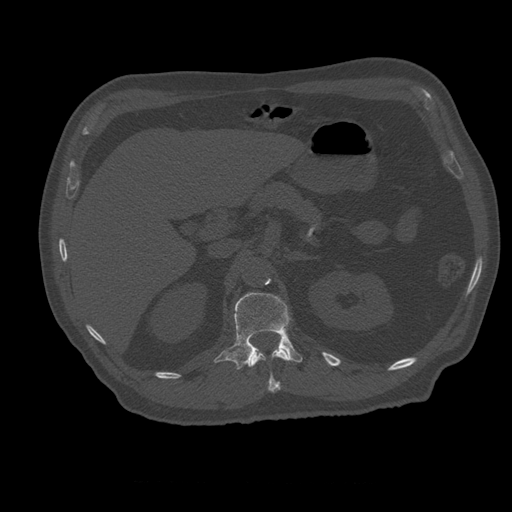
CT including the spine, one axial slice; position 245 of 399 along the scan axis; 120 kVp; bone window (W 1800 / L 400 HU); 1.25 mm slice thickness; 512 × 512 image matrix. Patient age 73 years. From the clinical record (not read from this slice): primary cancer: prostate.
Structures marked on this image (semi-automatically segmented with operator editing):
- L1 vertebra: bounding box (x1, y1, x2, y2) in pixels: (214, 293, 303, 370)
- T12 vertebra: (249, 347, 291, 393)